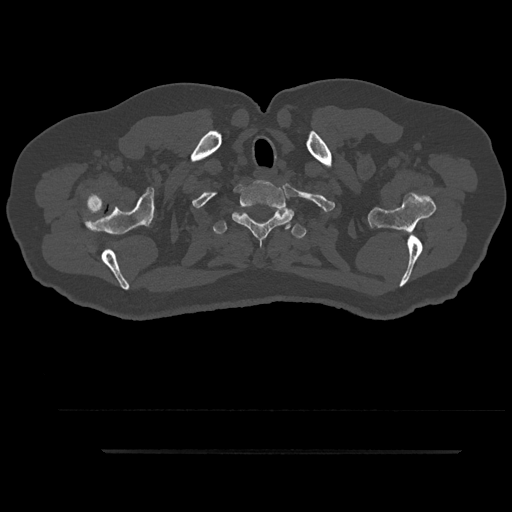
CT including the spine, one axial slice; position 790 of 797 along the scan axis; 120 kVp; bone window (W 1800 / L 400 HU); 0.5 mm slice thickness; 512 × 512 image matrix. Male patient, age 63 years. From the clinical record (not read from this slice): primary cancer: renal.
Outlined on this slice (semi-automatically segmented with operator editing):
- T1 vertebra: box from (x=232, y=185) to (x=295, y=245) px
- T2 vertebra: (x=213, y=212)–(x=306, y=239)